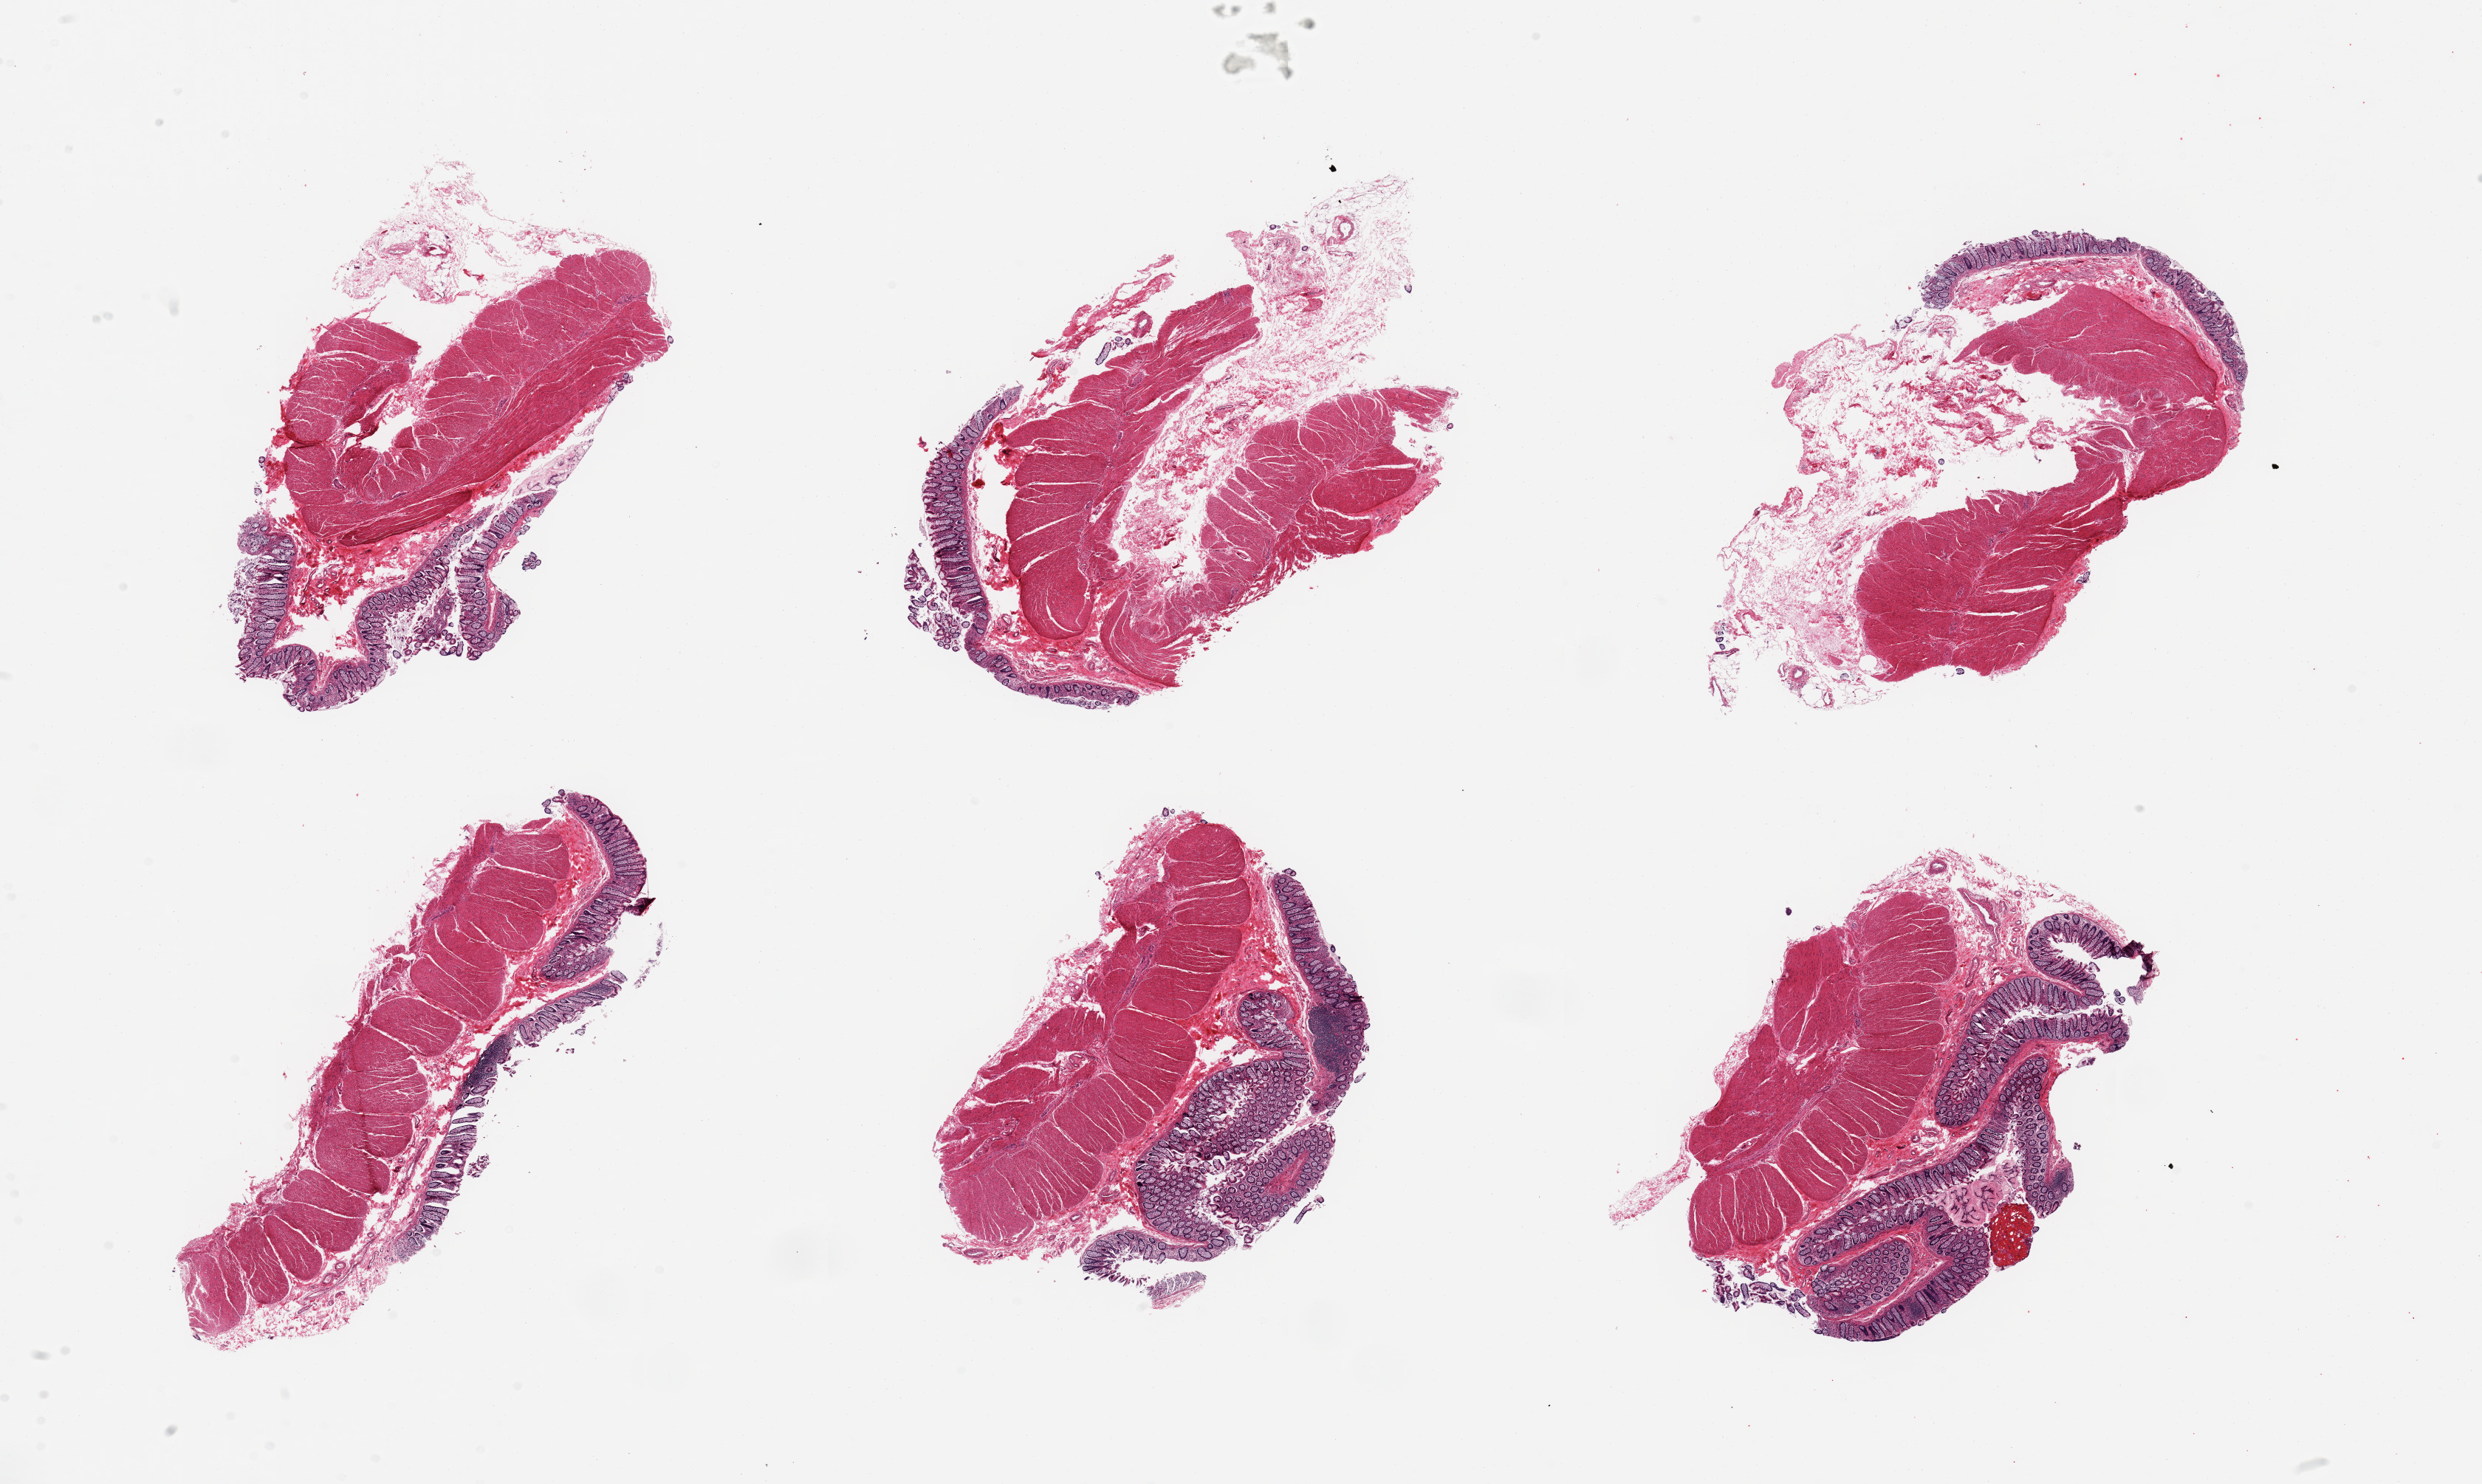
Digitized haematoxylin and eosin-stained section, brightfield — shown as a low-resolution overview of the whole scanned area (about 26.6 x 15.9 mm). PAXgene-fixed, paraffin-embedded tissue. Target tissue: transverse colon. Tissue donor sample.
Reviewer comment on this tissue sample: 6 pieces, mucosa well preserved up to ~0.4mm, ~10-20% thickness.